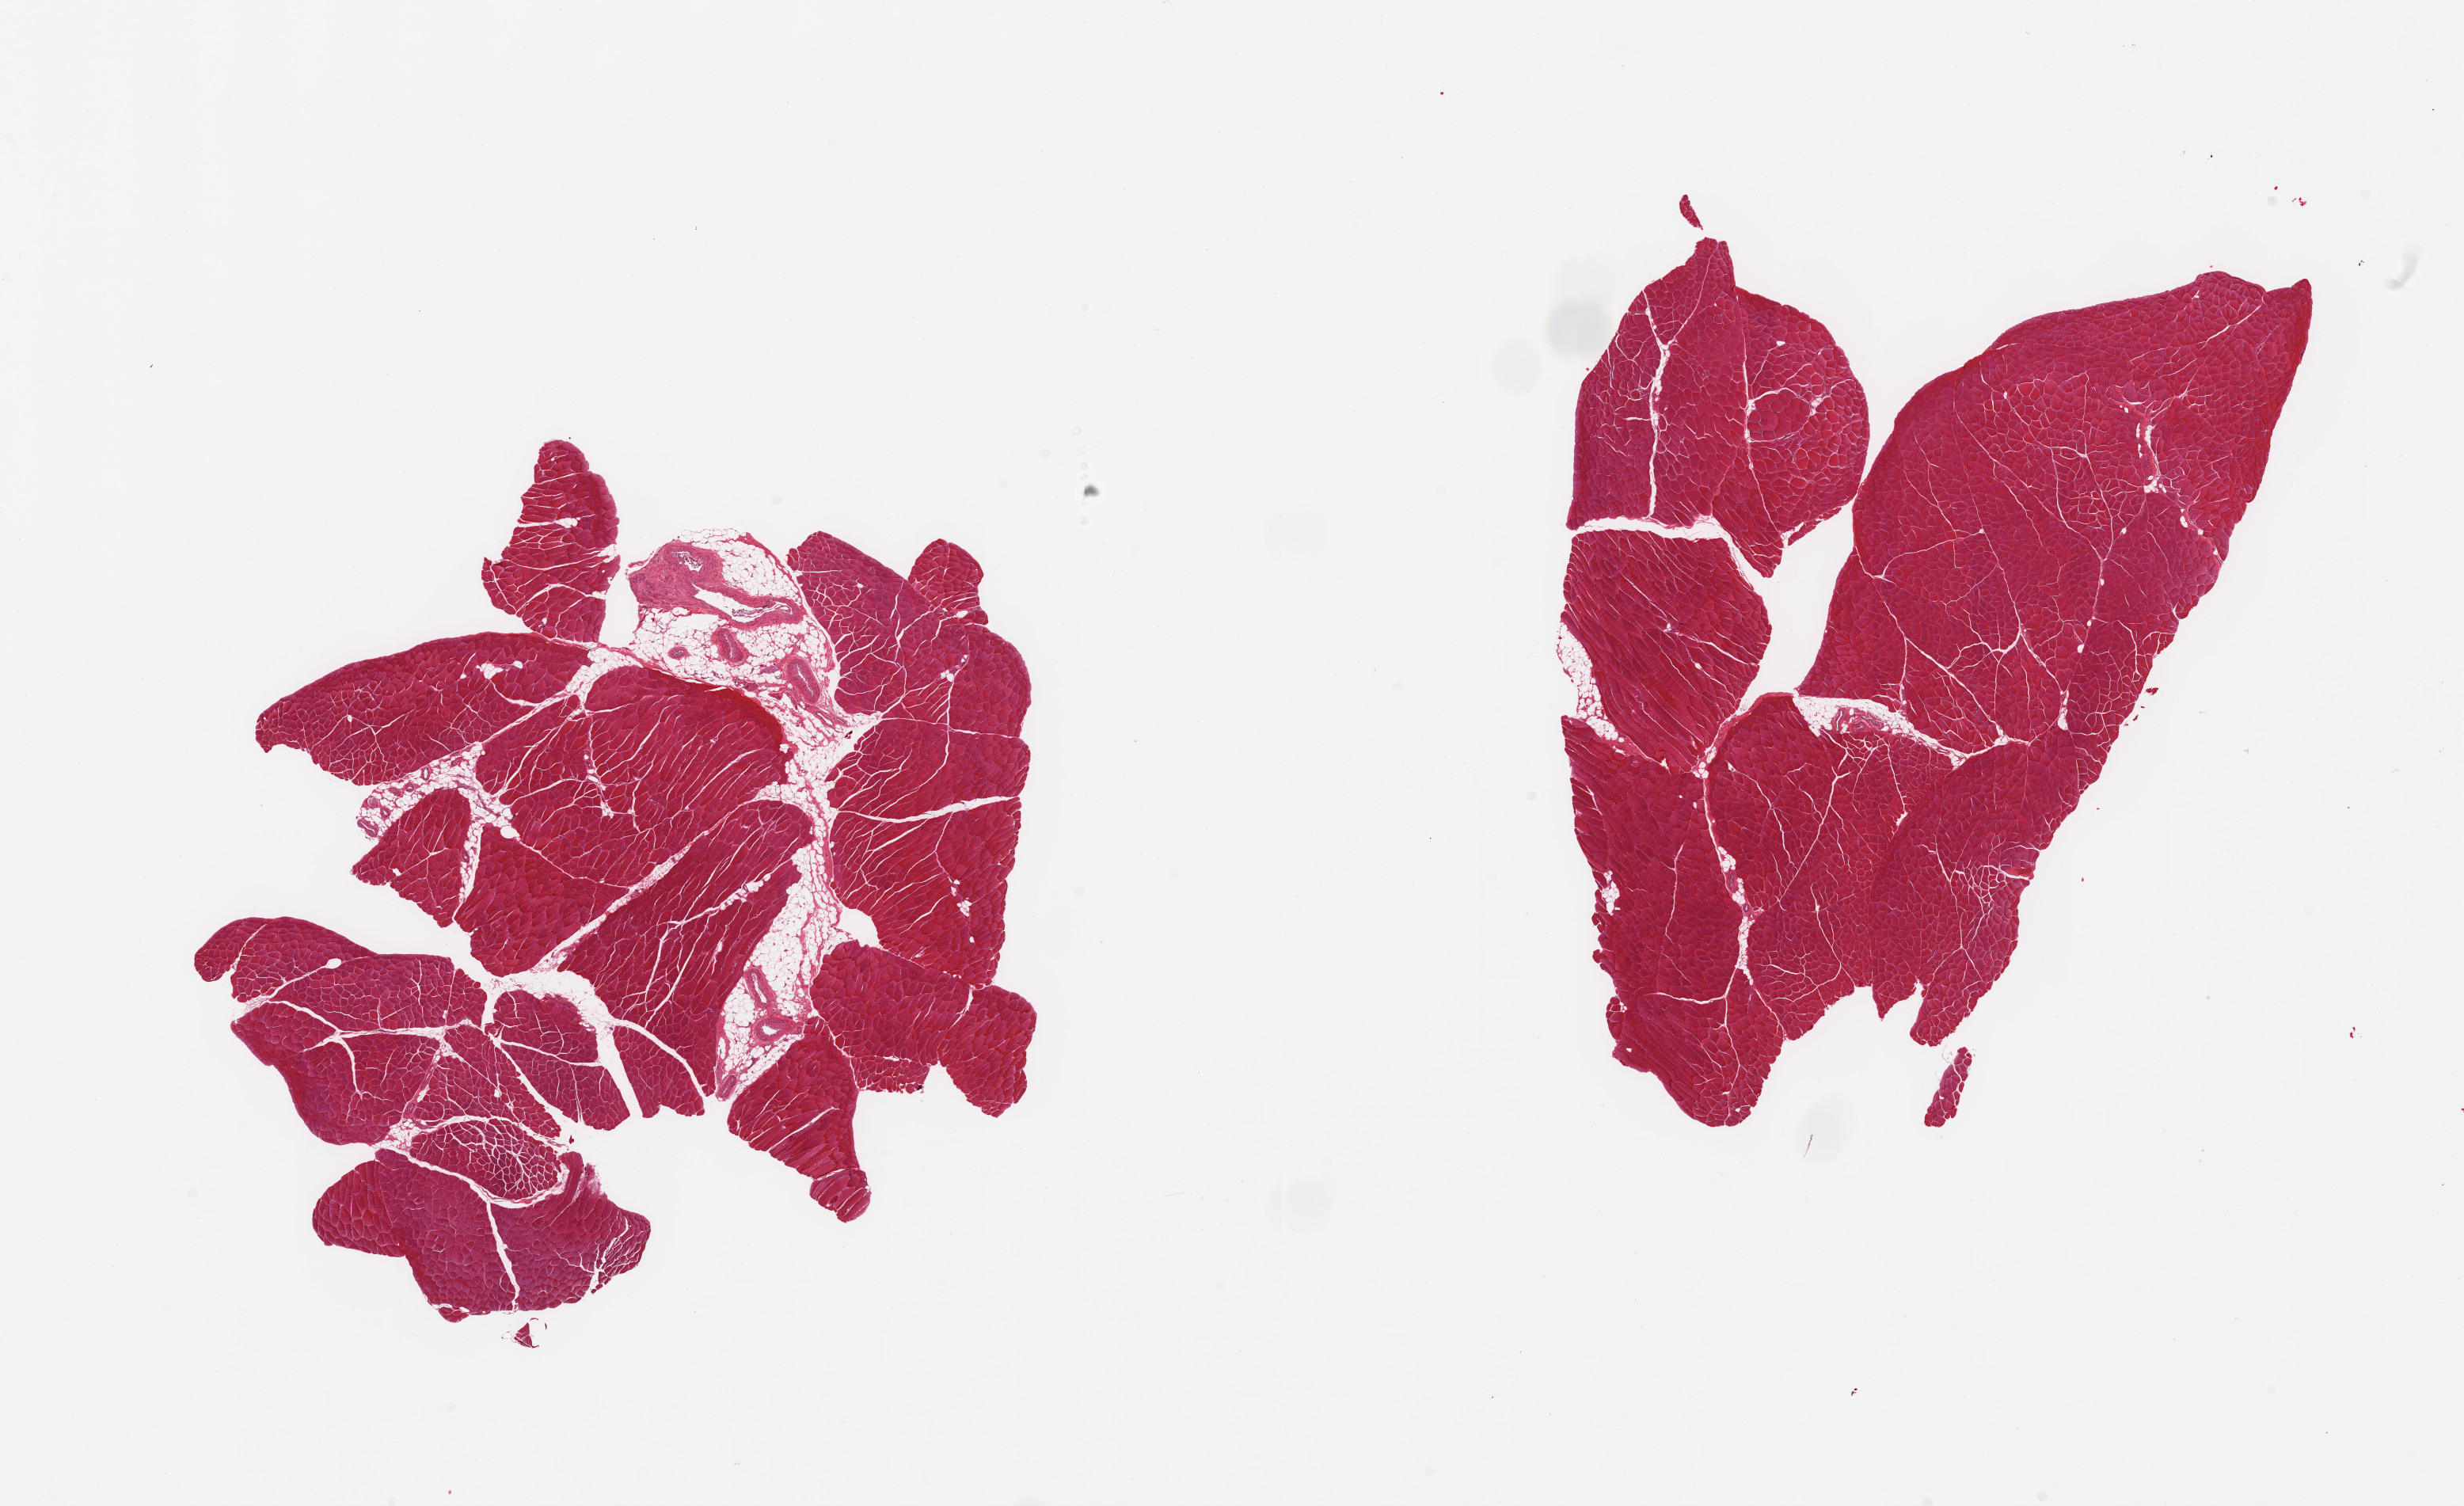
Whole-slide image, hematoxylin and eosin (H&E) stain — whole scanned area (about 24.6 x 15.0 mm) shown as a low-resolution overview; PAXgene-fixed, paraffin-embedded tissue; target tissue: skeletal muscle; tissue donor sample.
- reviewer comment on this tissue sample: 2 pieces, interstitial fat/vascular elements are 10-15% of tissue